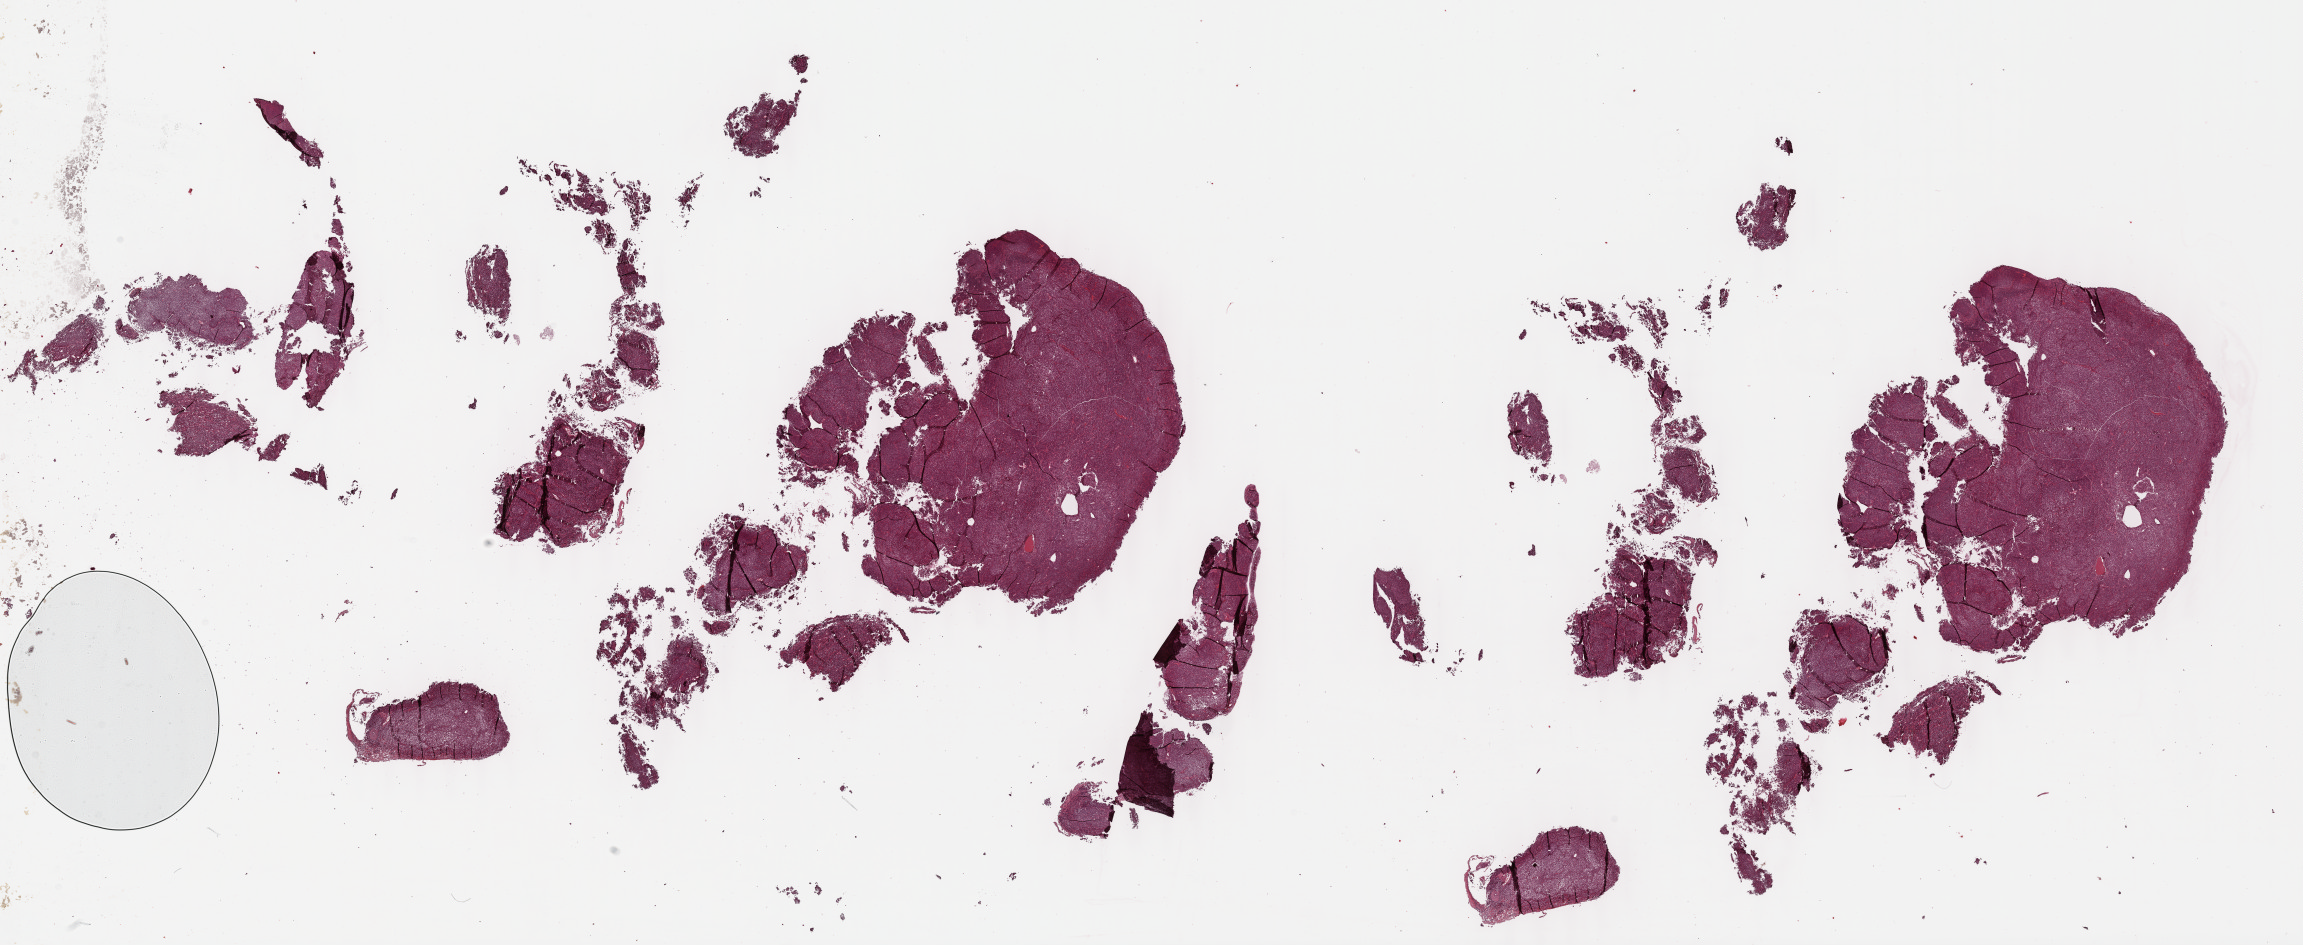
H&E-stained whole-slide image, shown as a low-resolution overview of the whole scanned area (about 37.2 x 15.3 mm, from a 40x scan). Formalin-fixed paraffin-embedded (FFPE) diagnostic section. Cervix, primary tumour sample. Patient: female, age at initial diagnosis 35 years. Histologic grade: G3 (poorly differentiated).
* pathologic diagnosis: Squamous cell carcinoma, NOS (cervix uteri)
* FIGO stage: IB2